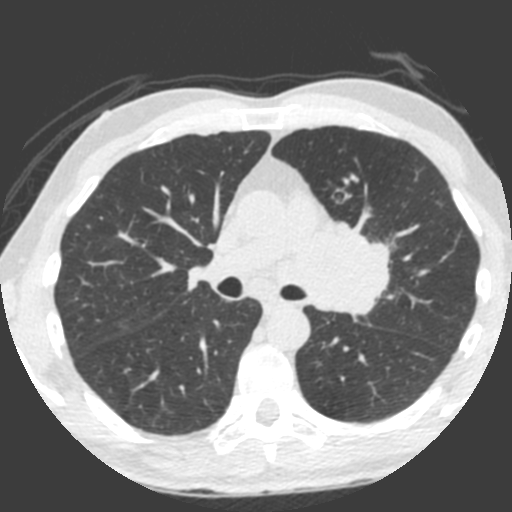
Low-dose screening chest CT, axial slice. Third screening round (two years after baseline). Lung window (W 1500 / L -600 HU). Standard (soft-tissue) reconstruction kernel (B). 120 kVp. Slice 135 of 212 in the series. 512 × 512 image matrix. Male participant, aged 55 years at enrolment. Current smoker at enrolment.
Expert-annotated lung lesion, box from (x=309, y=218) to (x=398, y=325) px. Screening reader's record for this exam (one nodule recorded; not confirmed to be the boxed lesion): non-calcified nodule or mass ≥4 mm, left upper lobe, 49 × 29 mm, spiculated (stellate) margins, soft tissue attenuation, pre-existing on the prior screen: yes; interval growth: yes. Participant outcome: lung cancer diagnosed 0 days after this screen — small cell carcinoma, NOS, left upper lobe, undifferentiated (G4), stage IV (AJCC 6th edition), 60 mm at pathology.